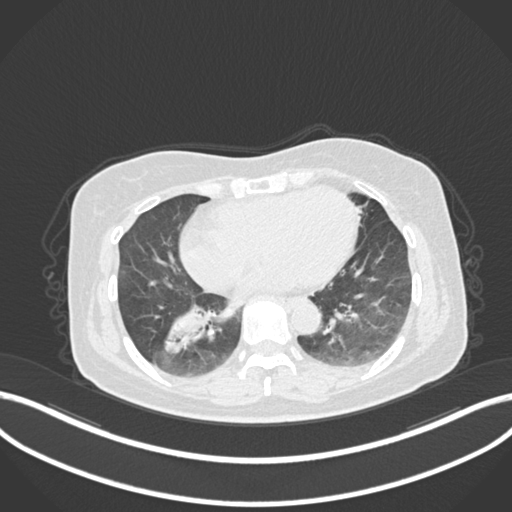
Chest CT, one axial slice; slice 51 of 222 in the series (ordered by position); lung window (W 1500 / L -600 HU); 512 × 512 image matrix. Patient: female, 67 years. Case-level facts recorded for this patient, not image findings: clinical TNM (as recorded): T1c N1 M0.
Structures marked on this image (bounding box drawn by a radiologist):
- lung tumour (recorded histology: adenocarcinoma): bounding box <159,296,226,359> (left, top, right, bottom; pixels)